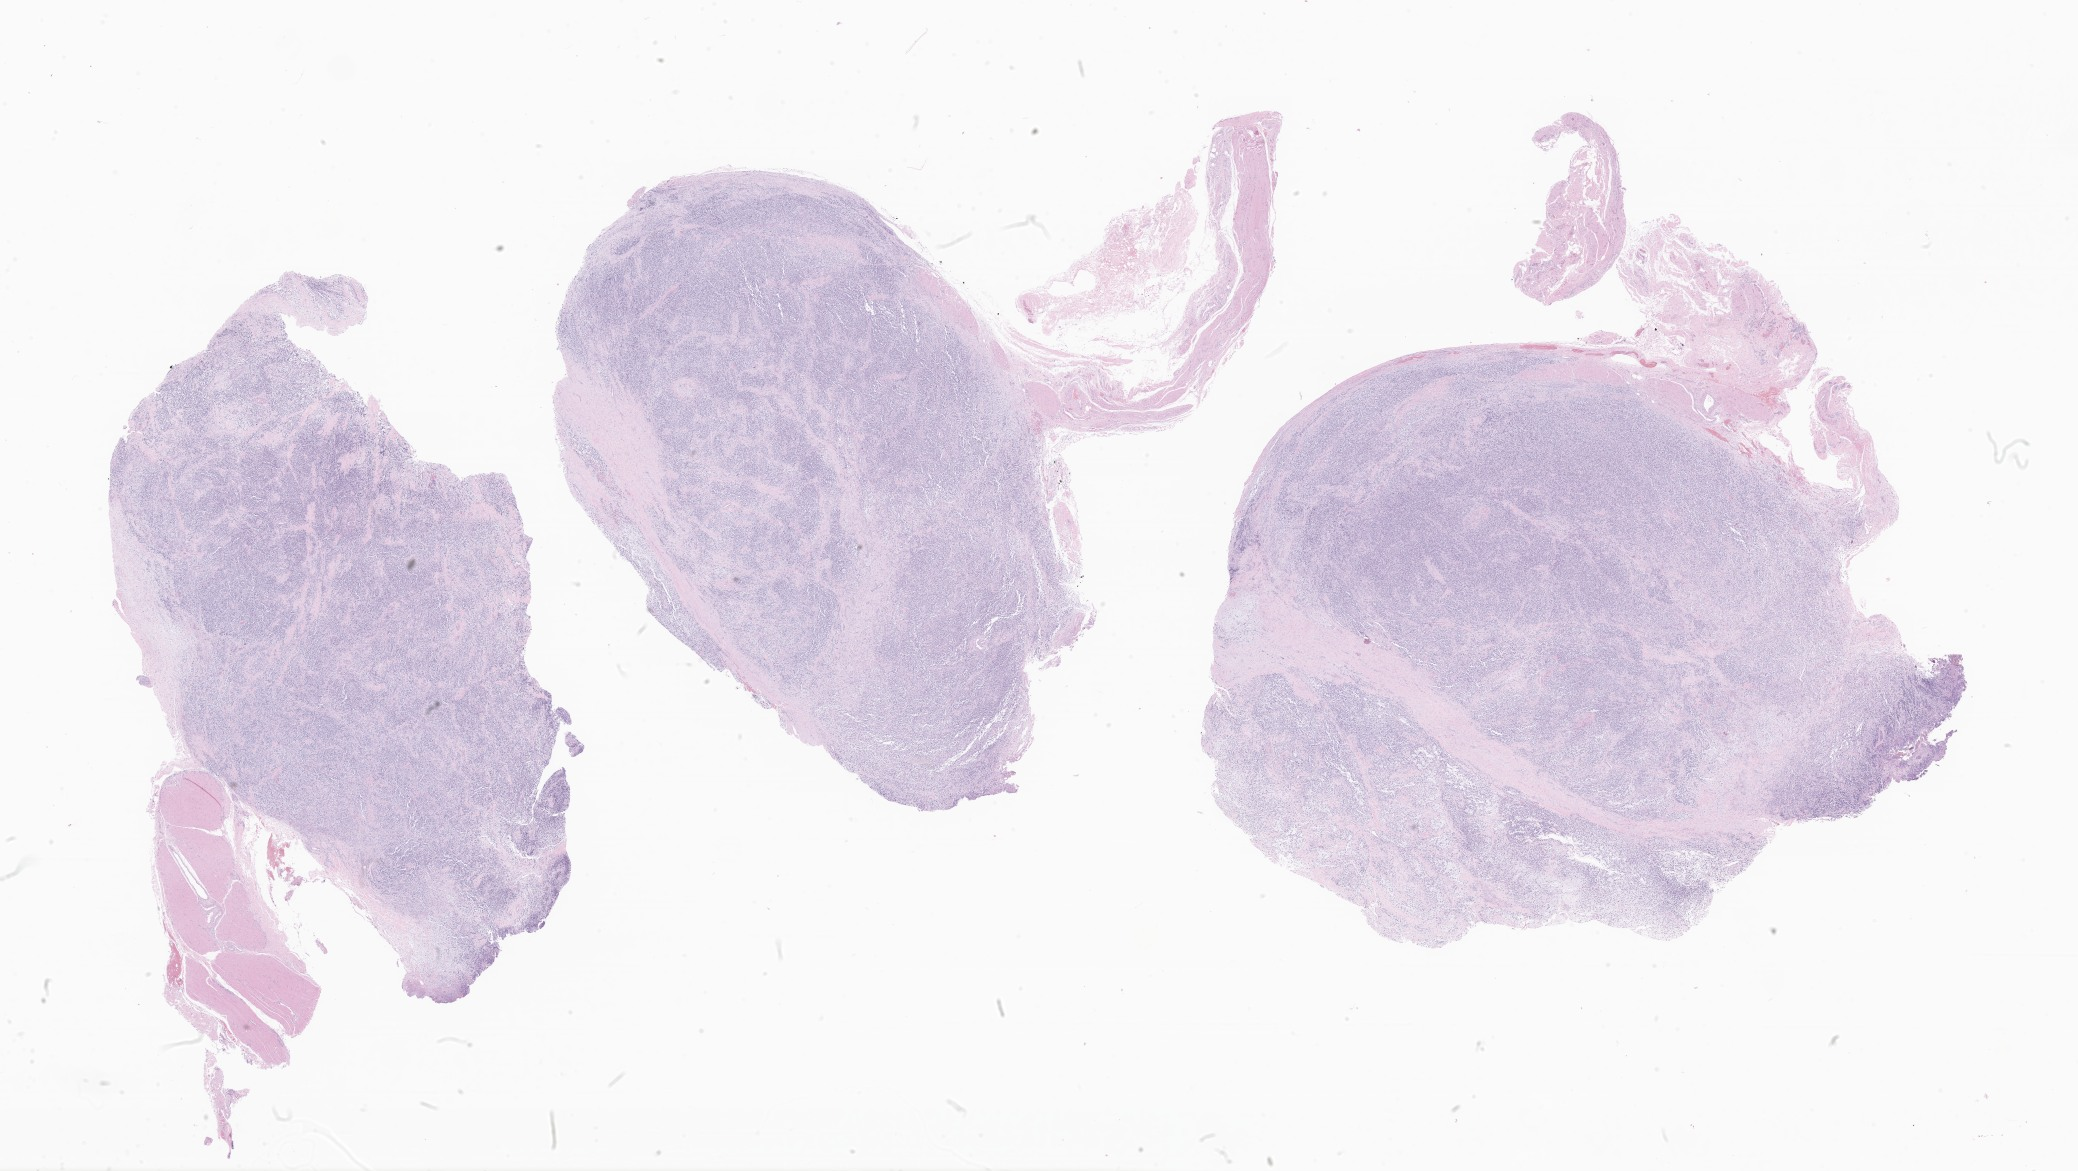
Whole-slide image, haematoxylin and eosin stain of tumor tissue from the testis, shown as a low-resolution overview of the whole scanned area (about 35.1 x 19.8 mm); formalin-fixed paraffin-embedded section. Male patient, age 213 months.
Diagnosis: Rhabdomyoma, NOS.